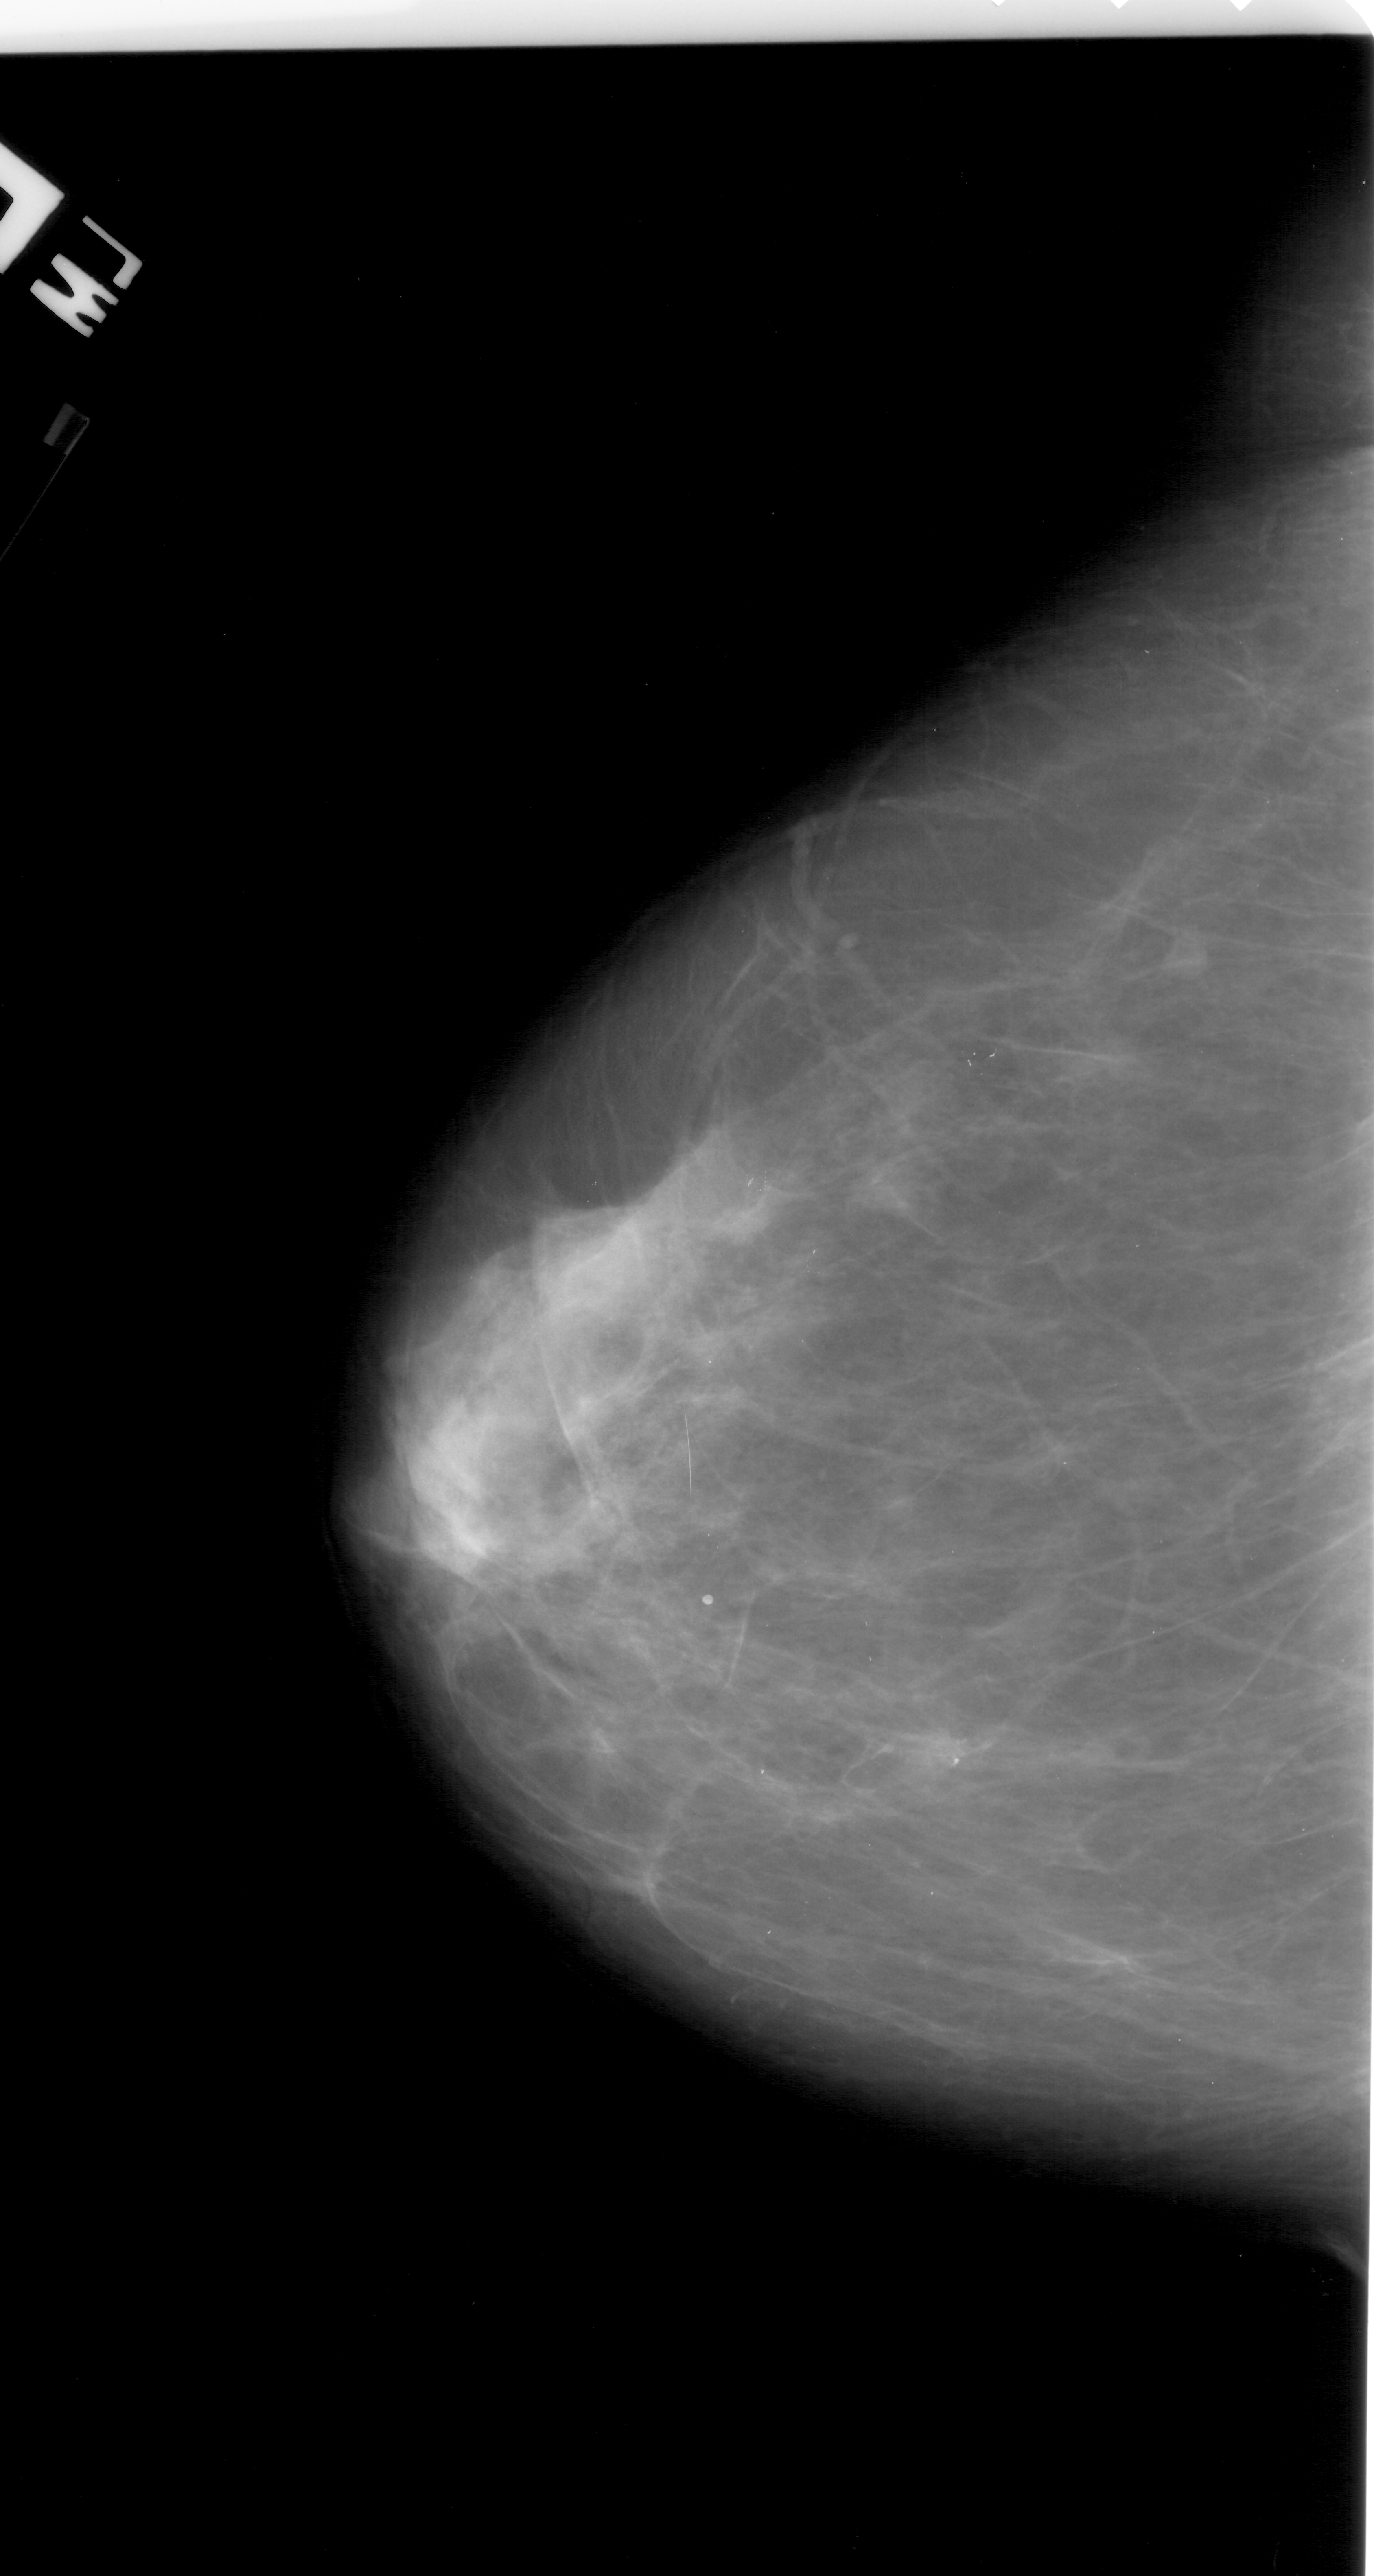
Scanned film-screen mammogram; left breast; craniocaudal (CC) view; breast composition: scattered fibroglandular densities (BI-RADS density category 2 of 4).
Radiologist-marked abnormalities on this image: calcifications, morphology pleomorphic, distribution linear; BI-RADS assessment category 4; subtlety rating 1 on a 1 (subtle) to 5 (obvious) scale; pathology result (as recorded, not read from the image): malignant.